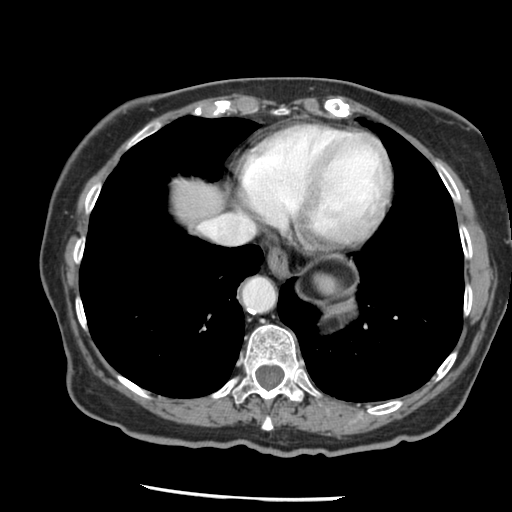
Contrast-enhanced abdominal CT, one axial slice. Intravenous contrast given. Soft-tissue window (W 400 / L 40 HU). 2.5 mm slice thickness. 512 × 512 image matrix, field of view 330 × 330 mm. Female patient, age 85 years. Case-level facts recorded for this patient, not image findings: diagnosis: colorectal cancer liver metastases, imaged before liver resection.
Outlined on this slice (manually delineated by an expert):
- hepatic veins: bounding box <200,215,235,243> (left, top, right, bottom; pixels)
- liver: <169,180,224,225>
- planned liver remnant (the part of the liver to remain after resection): <169,180,224,225>